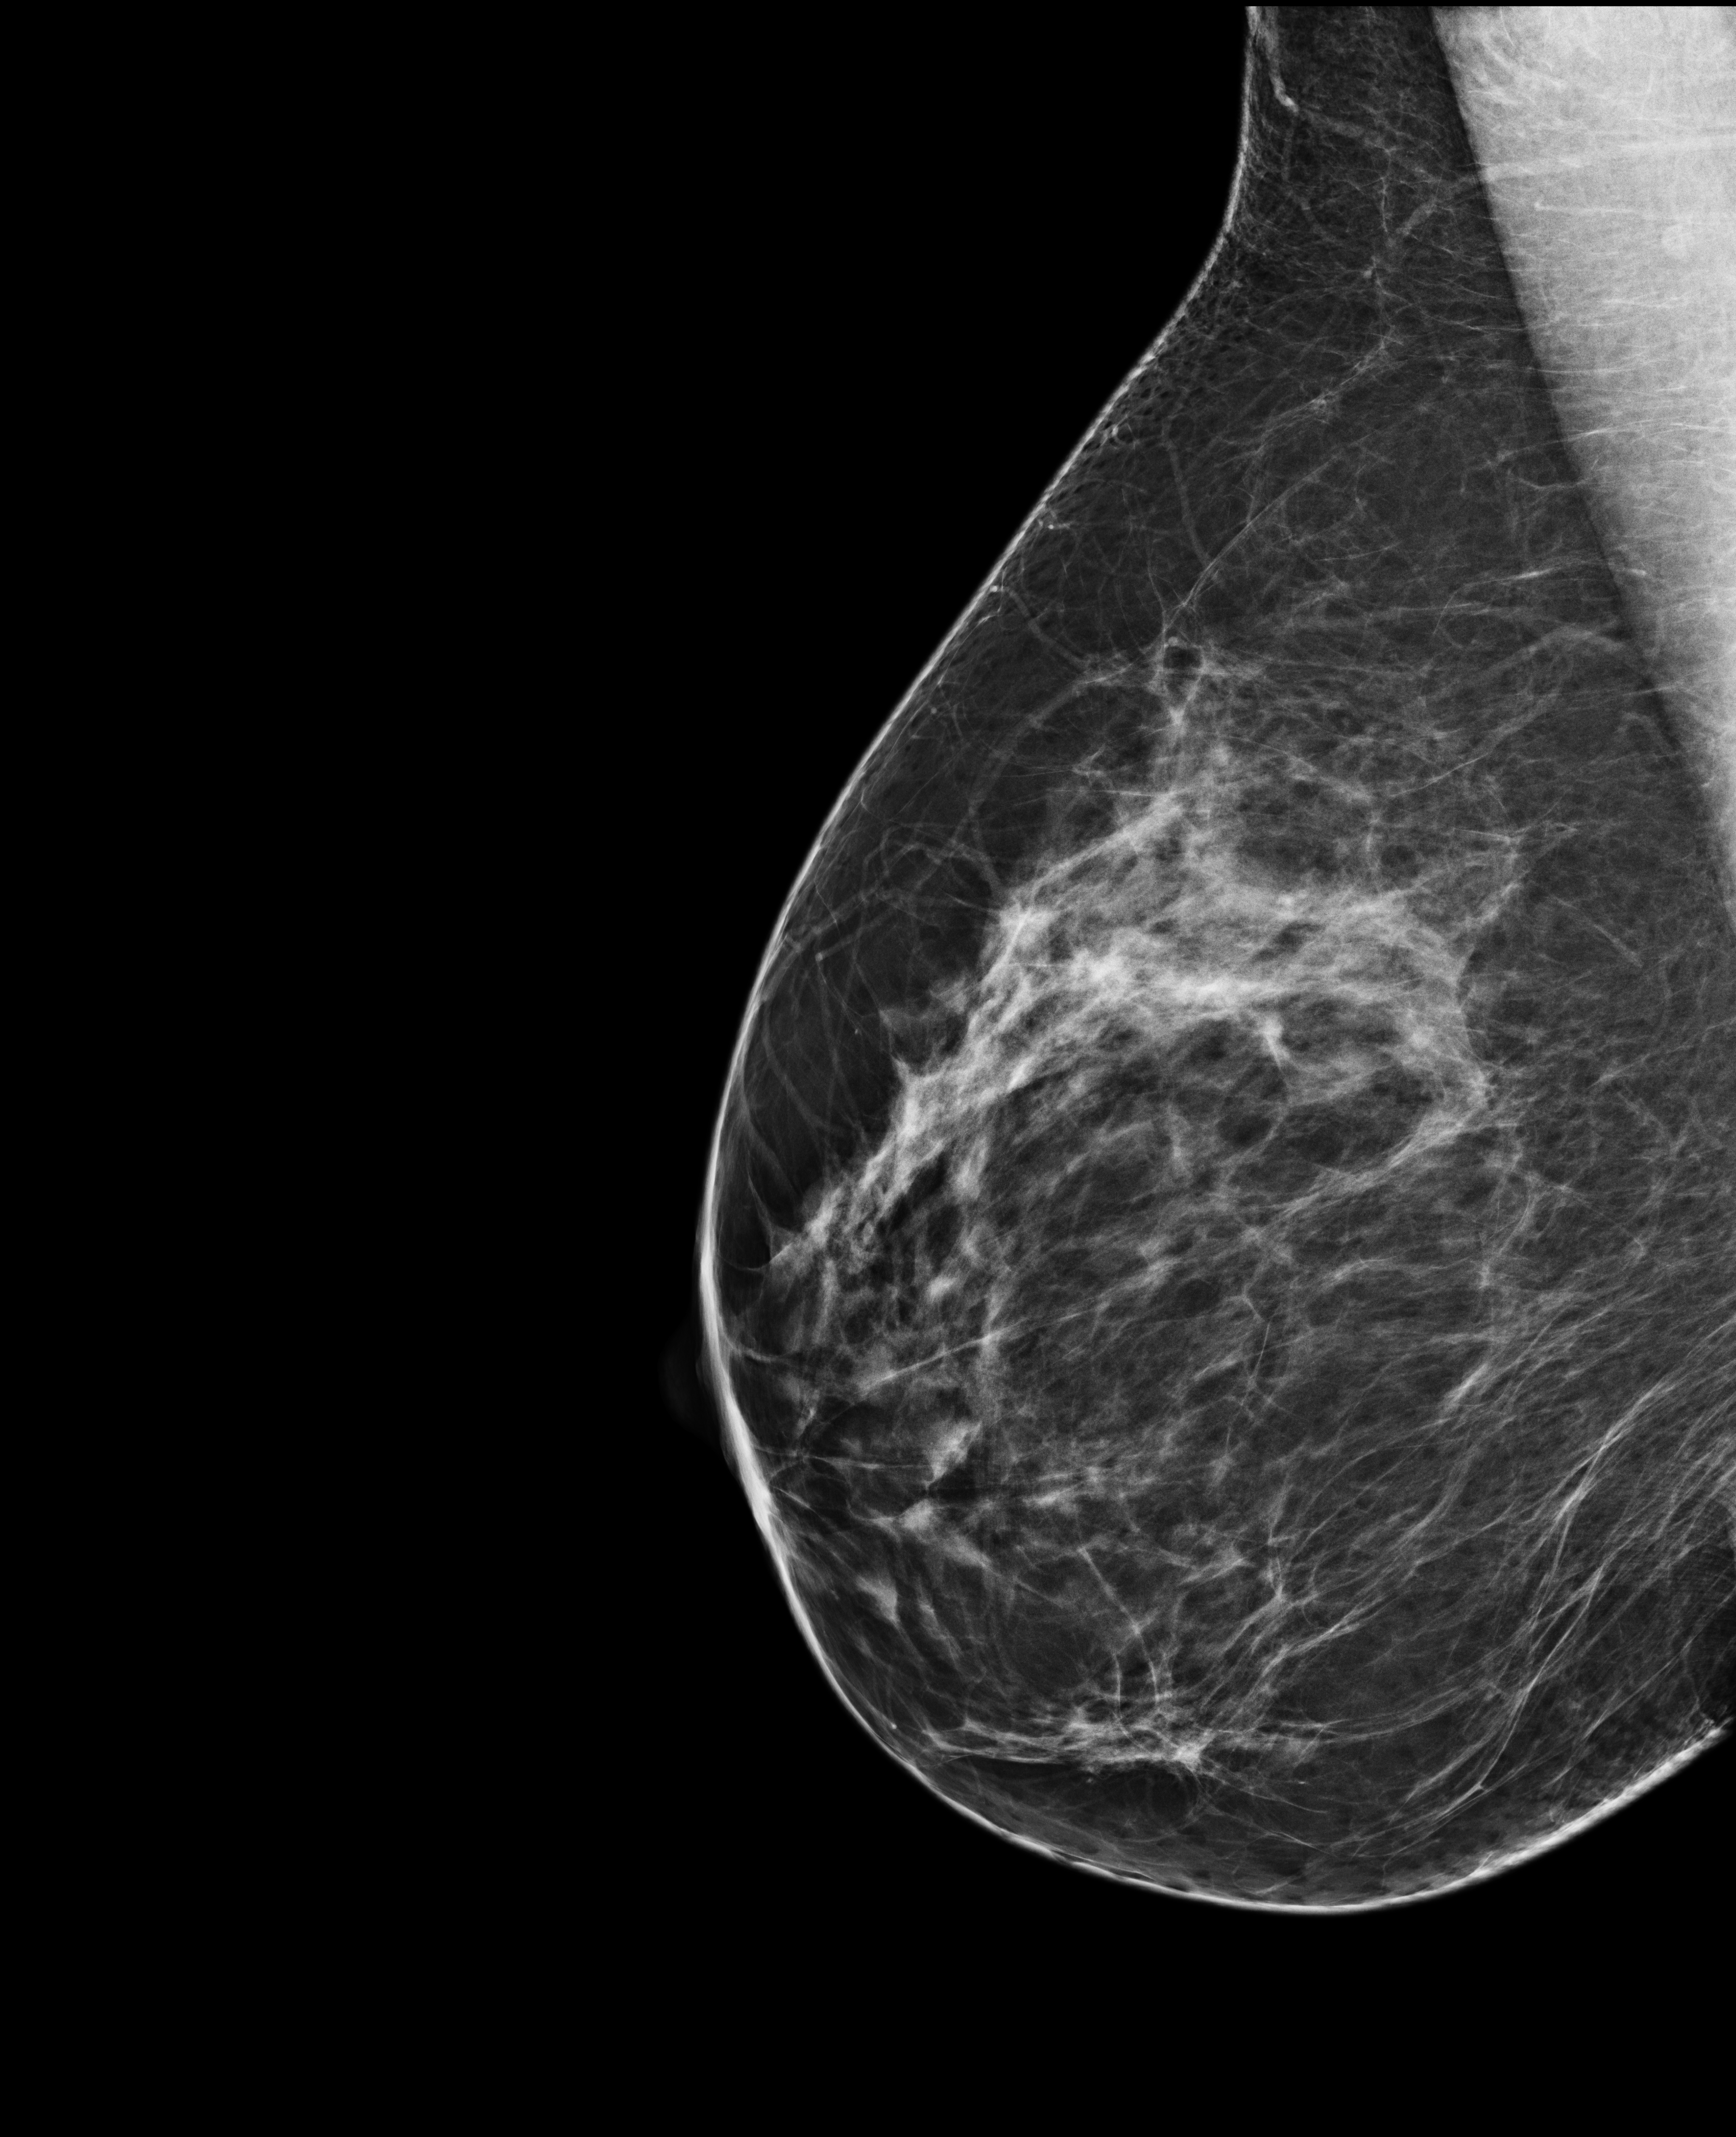
Screening examination, system: Selenia Dimensions. Patient aged 50 years (female).
Image type: full-field digital mammogram. Breast: right. Projection: MLO view.